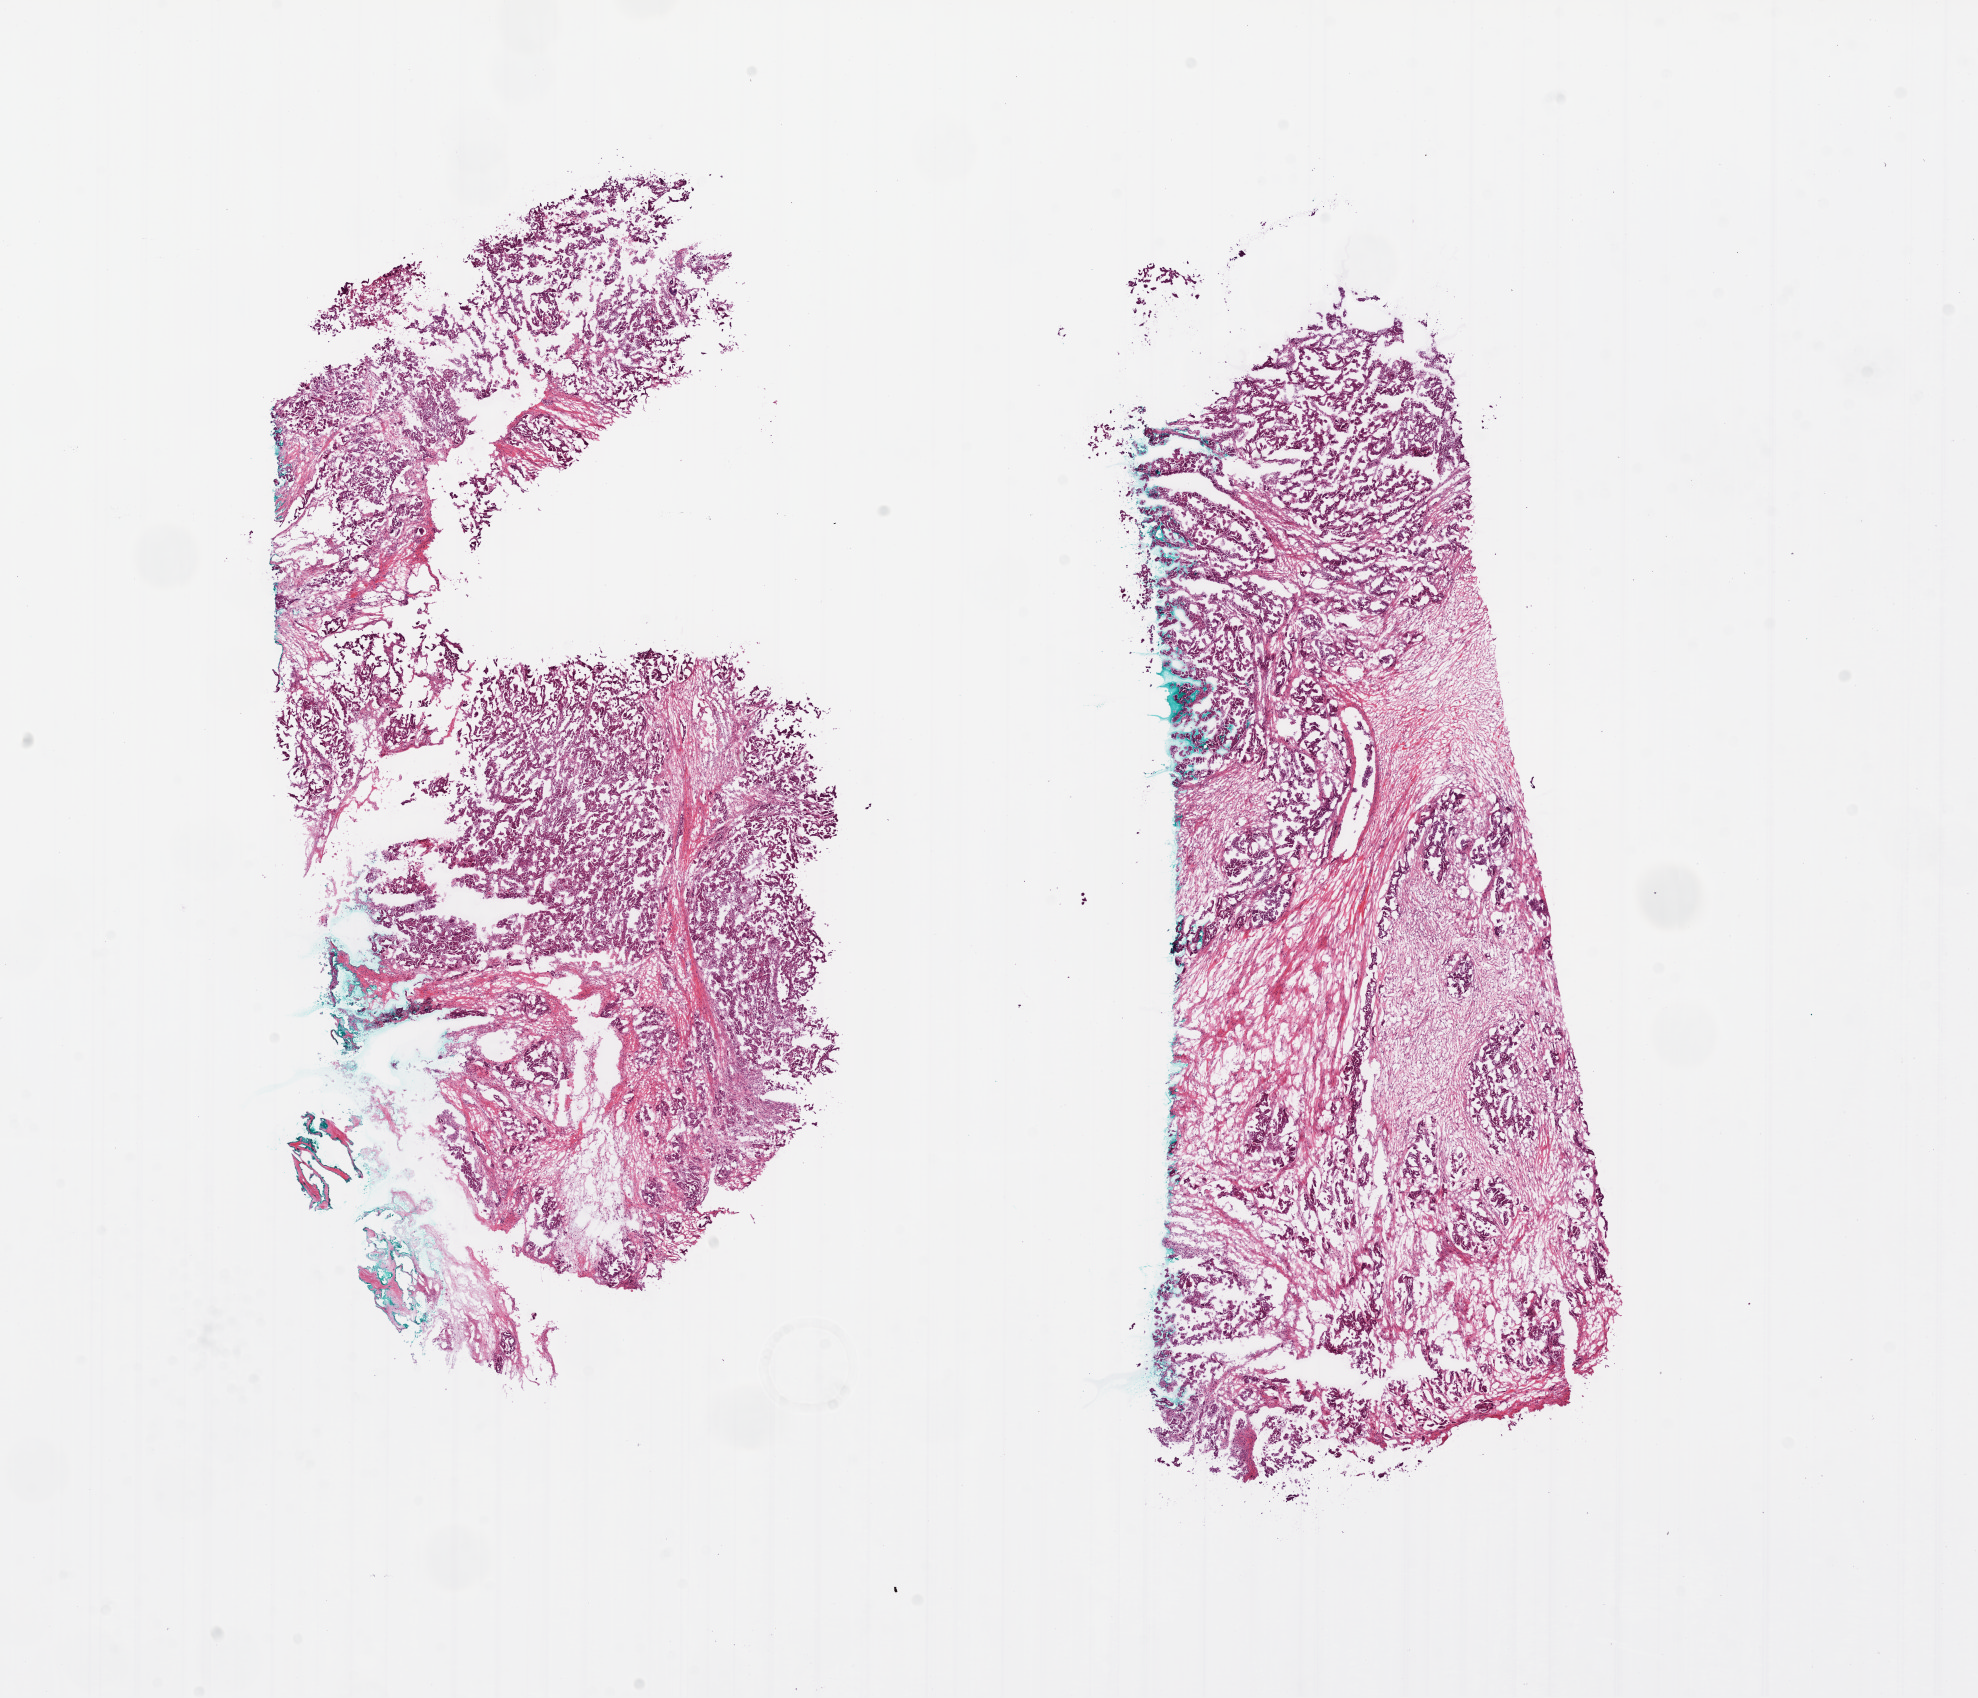
Digitized H&E-stained tissue section (whole slide), low-resolution overview of the scanned area, about 16.0 x 13.7 mm (acquisition: 20x scan). Frozen section from the bottom of the tissue portion. Sample: primary tumour, ovary. Patient: female, age at initial diagnosis 55 years. Histologic grade: GX (grade cannot be assessed). Pathologist review of this section (percent, as recorded): tumour cells 60%, tumour nuclei 80%, normal cells 0%, stromal cells 40%, necrosis 0%.
Laterality: bilateral. FIGO stage: IIIC. Diagnosis: Serous cystadenocarcinoma, NOS.